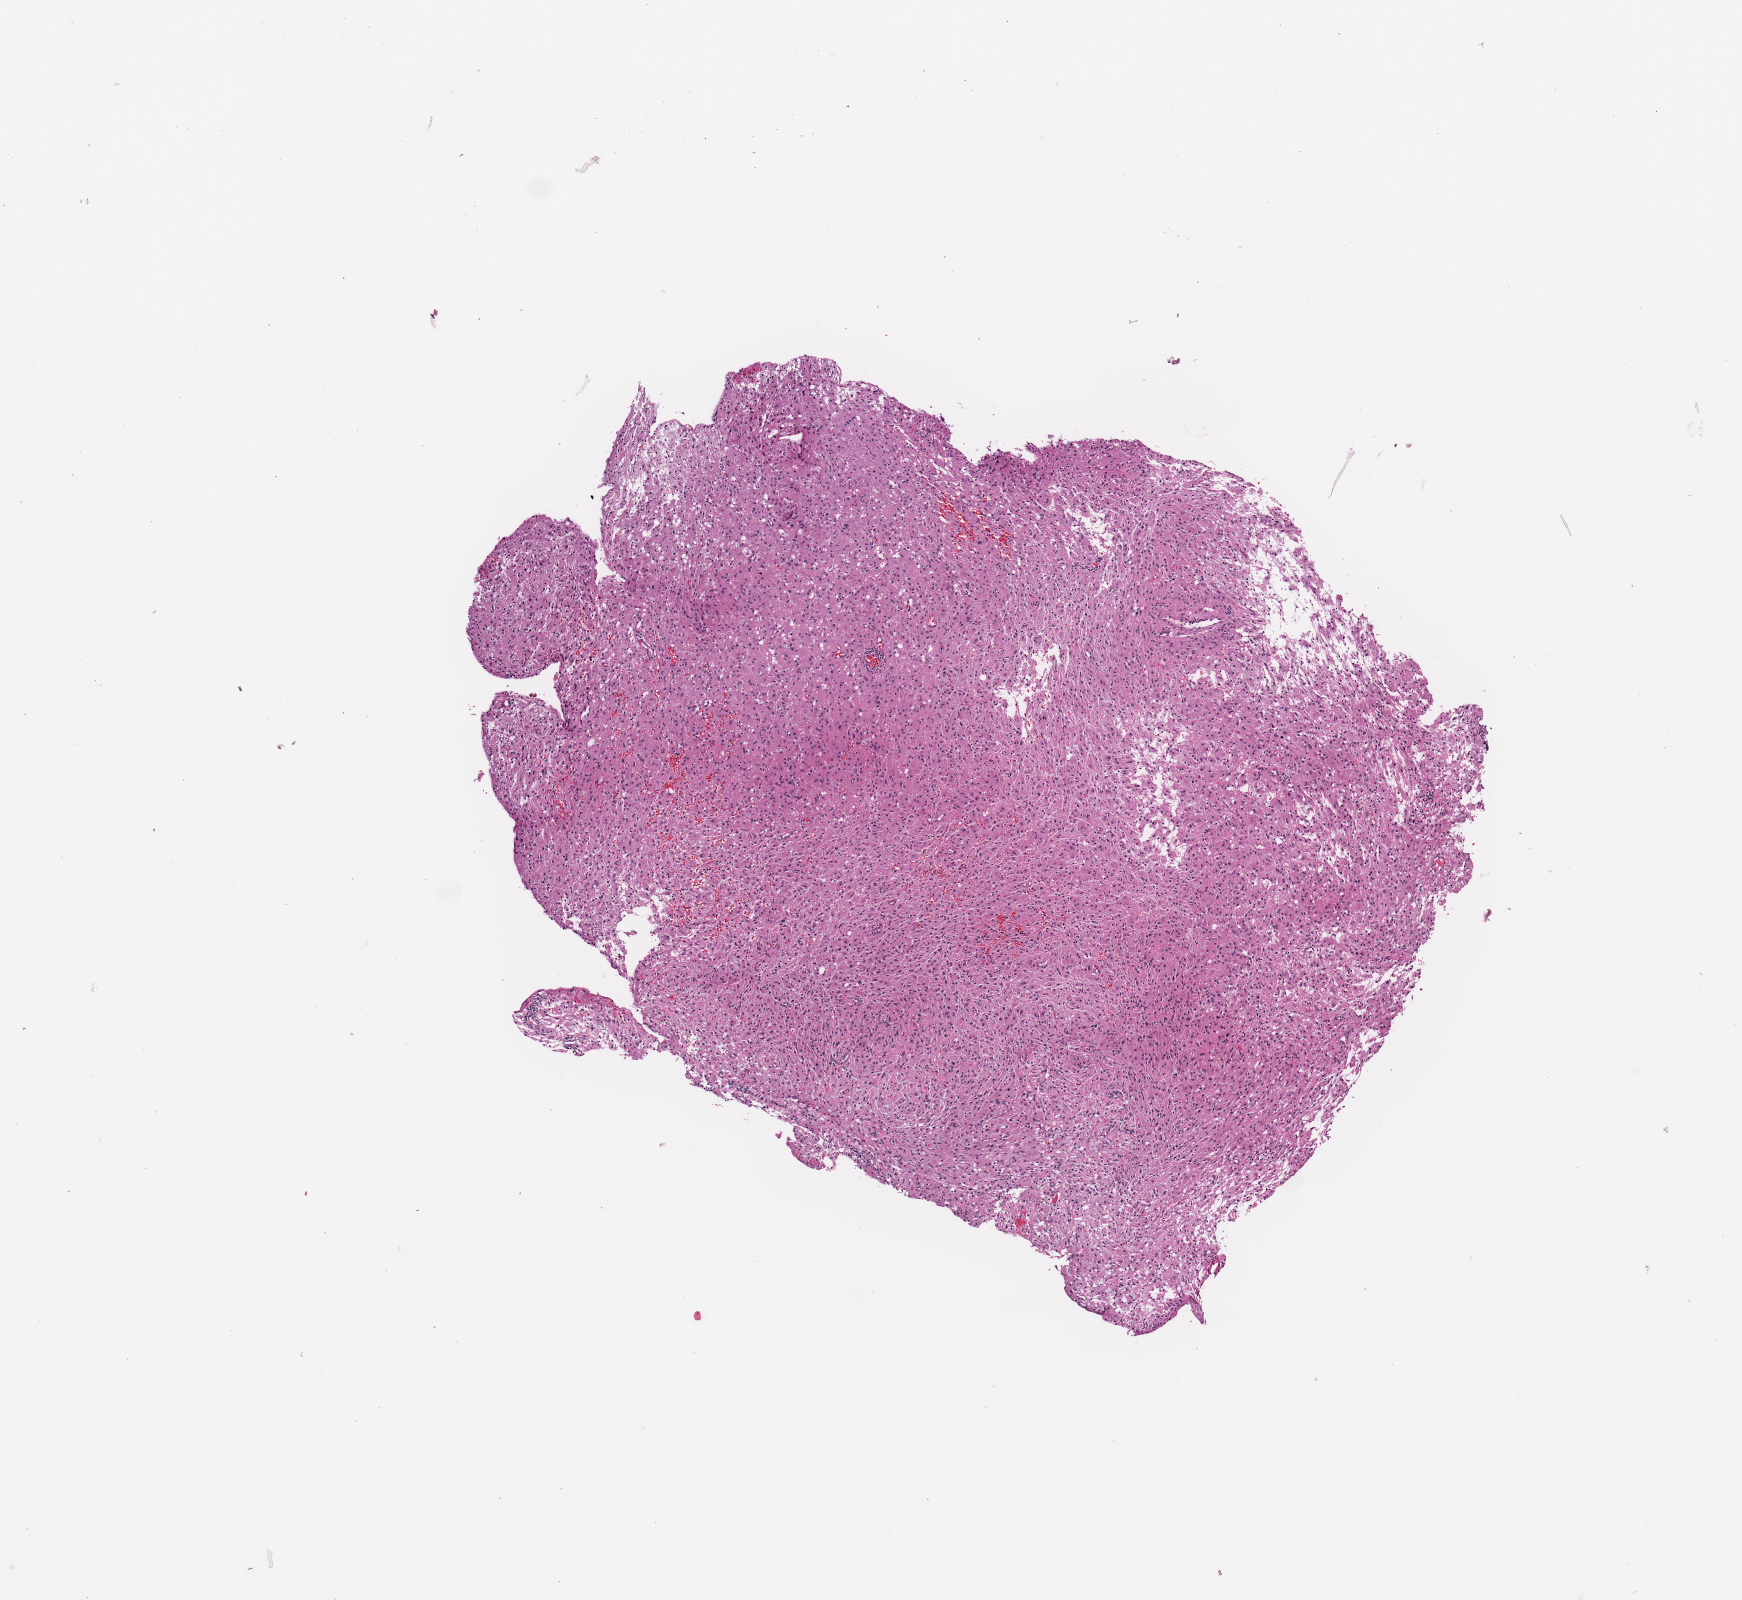
Hematoxylin and eosin (H&E) stained whole-slide image, low-resolution overview of the scanned area, about 6.9 x 6.3 mm (slide scanned at 20x); tumour tissue sample, sampled site: brain. 50-year-old female patient. Pathologist review of this section (percent, as recorded): tumour nuclei 85%, necrosis 3%.
• diagnosis: Glioblastoma